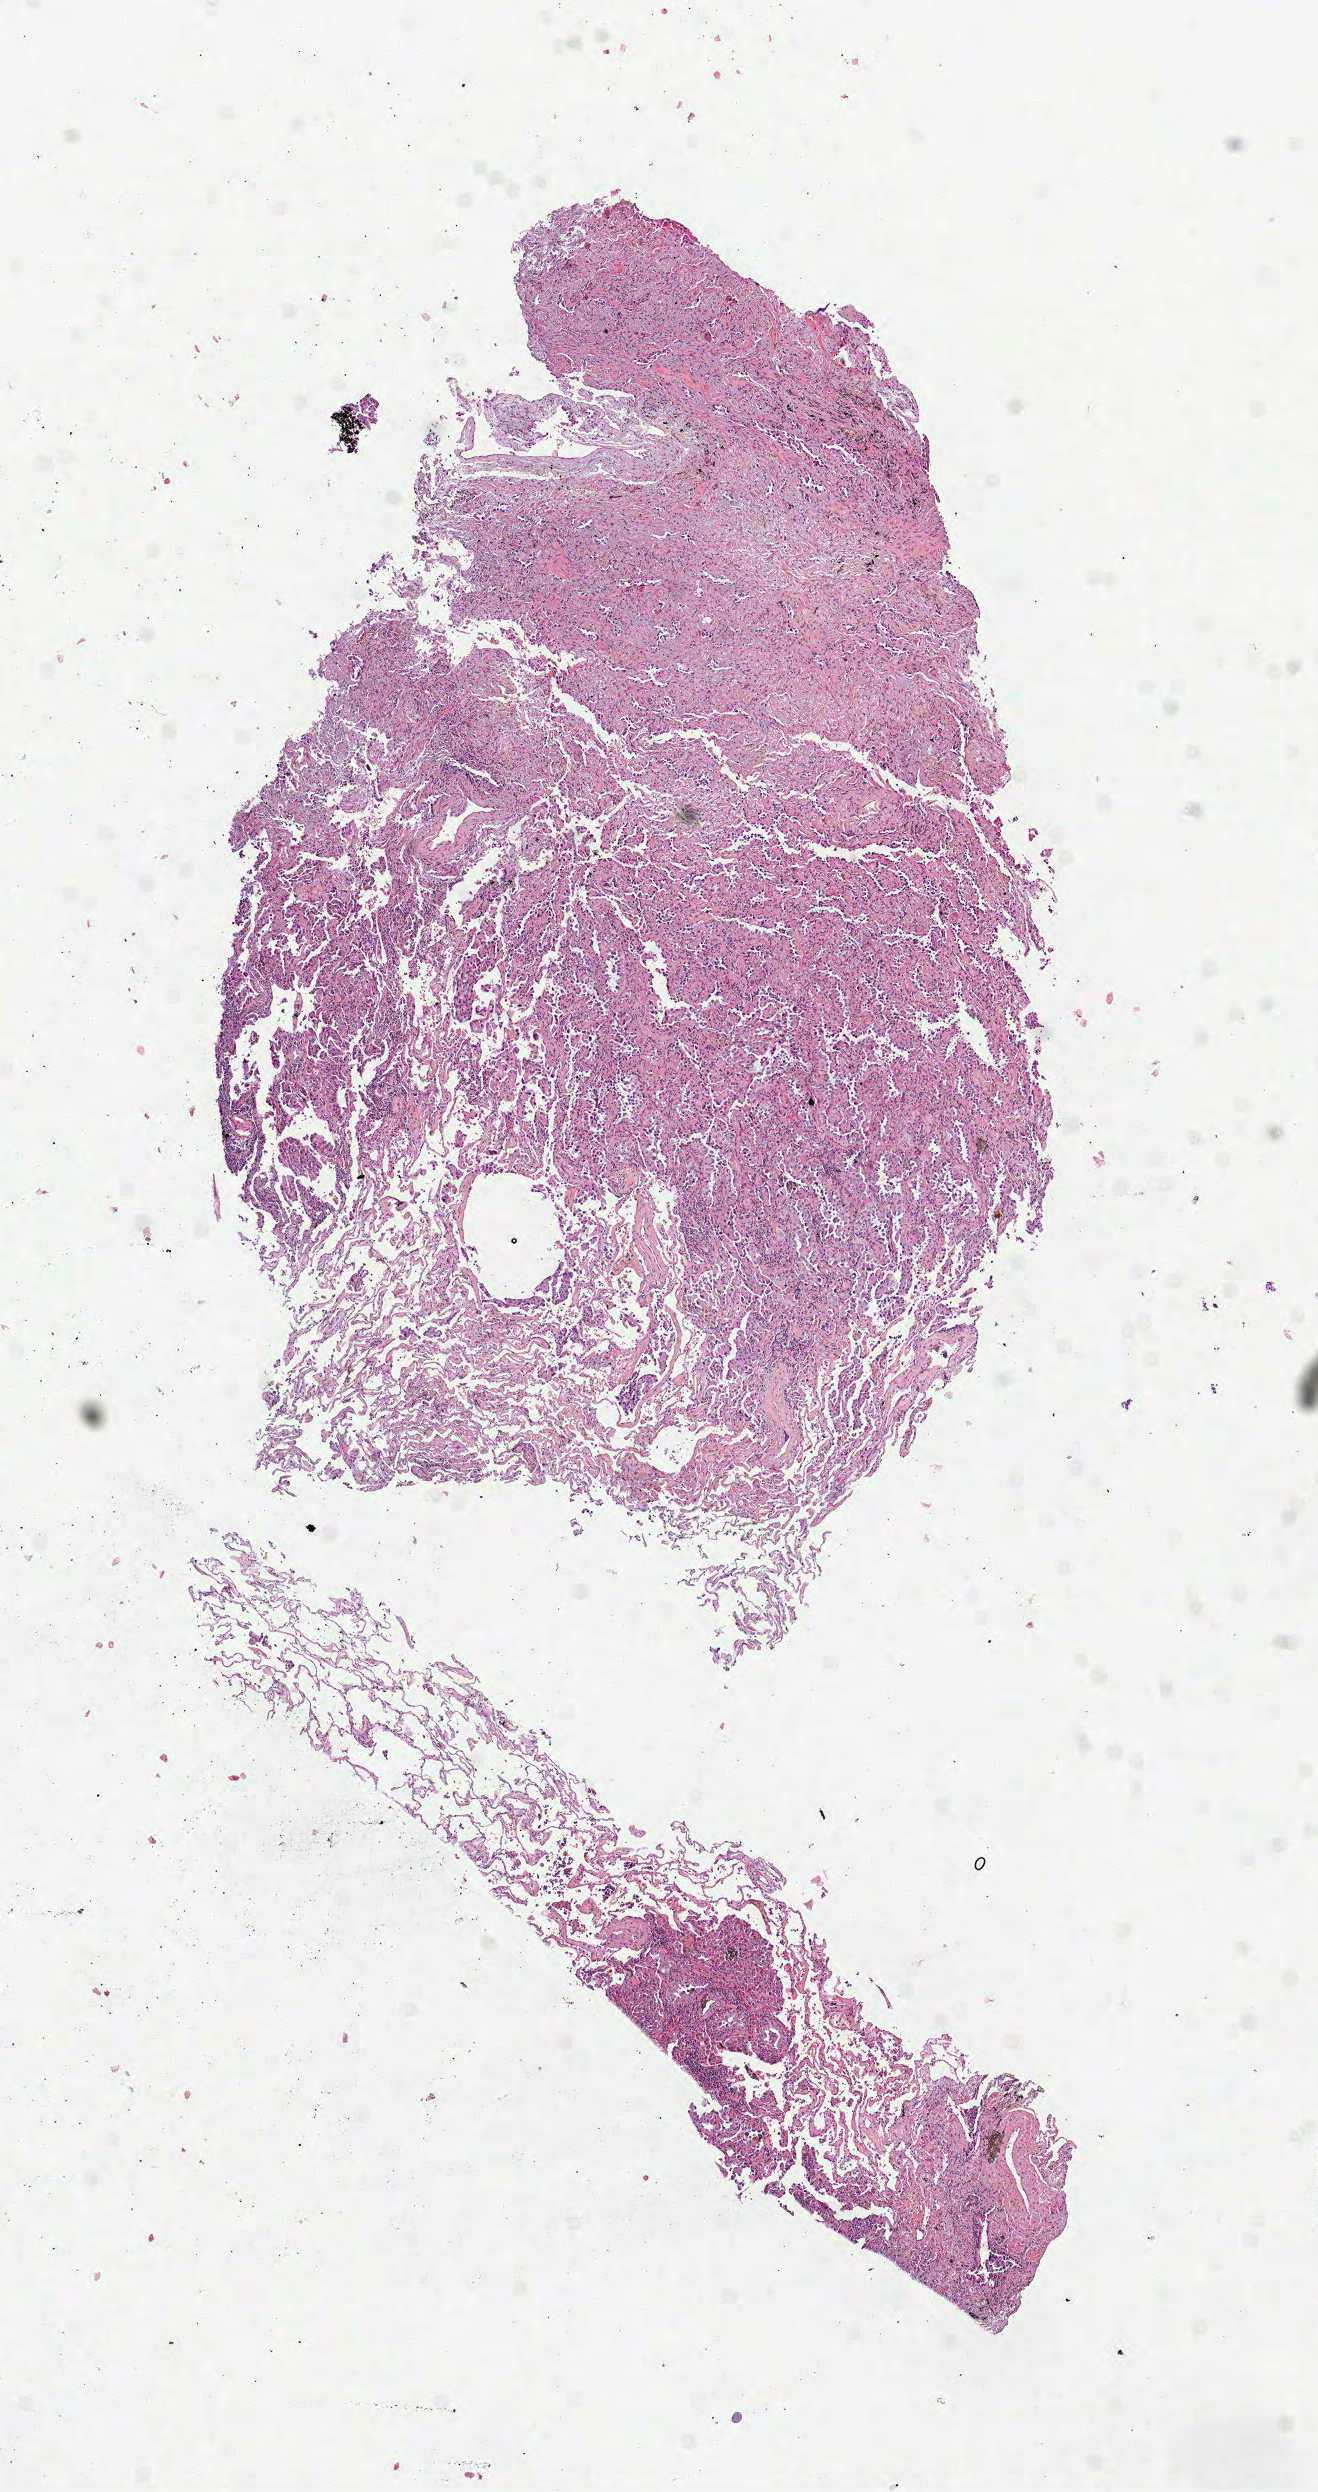
Digitized Hematoxylin and eosin (H&E) stained tissue section (whole slide) — low-resolution overview of the scanned area, about 5.3 x 10.1 mm (acquisition: 40x scan), FFPE section, primary tumour sample from the lung. Female, age 74 years at initial diagnosis.
Pathologic diagnosis: Bronchiolo-alveolar carcinoma, non-mucinous (lower lobe, lung).